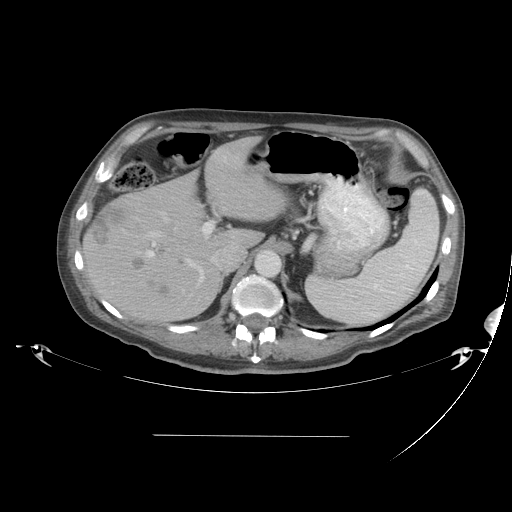
Contrast-enhanced abdominal CT, one axial slice; slice 29 of 48 in the series (ordered by position); reconstruction kernel STANDARD; intravenous contrast given; soft-tissue window (W 400 / L 40 HU); 5 mm slice thickness; 512 × 512 image matrix, field of view 486 × 486 mm. Male patient, age 65 years. From the clinical record (not read from this slice): diagnosis: colorectal cancer liver metastases, imaged before liver resection; multiple liver metastases: yes; largest metastasis: 11 cm; chemotherapy before resection: yes.
Annotated regions visible in this slice (manually delineated by an expert):
- hepatic veins: box from (x=136, y=212) to (x=185, y=294) px
- liver: (x=83, y=138)–(x=285, y=320)
- planned liver remnant (the part of the liver to remain after resection): (x=155, y=138)–(x=284, y=248)
- portal vein (with intrahepatic branches): (x=146, y=207)–(x=225, y=282)
- liver metastasis: (x=133, y=260)–(x=141, y=268)
- liver metastasis: (x=146, y=280)–(x=170, y=297)
- liver metastasis: (x=93, y=205)–(x=128, y=241)